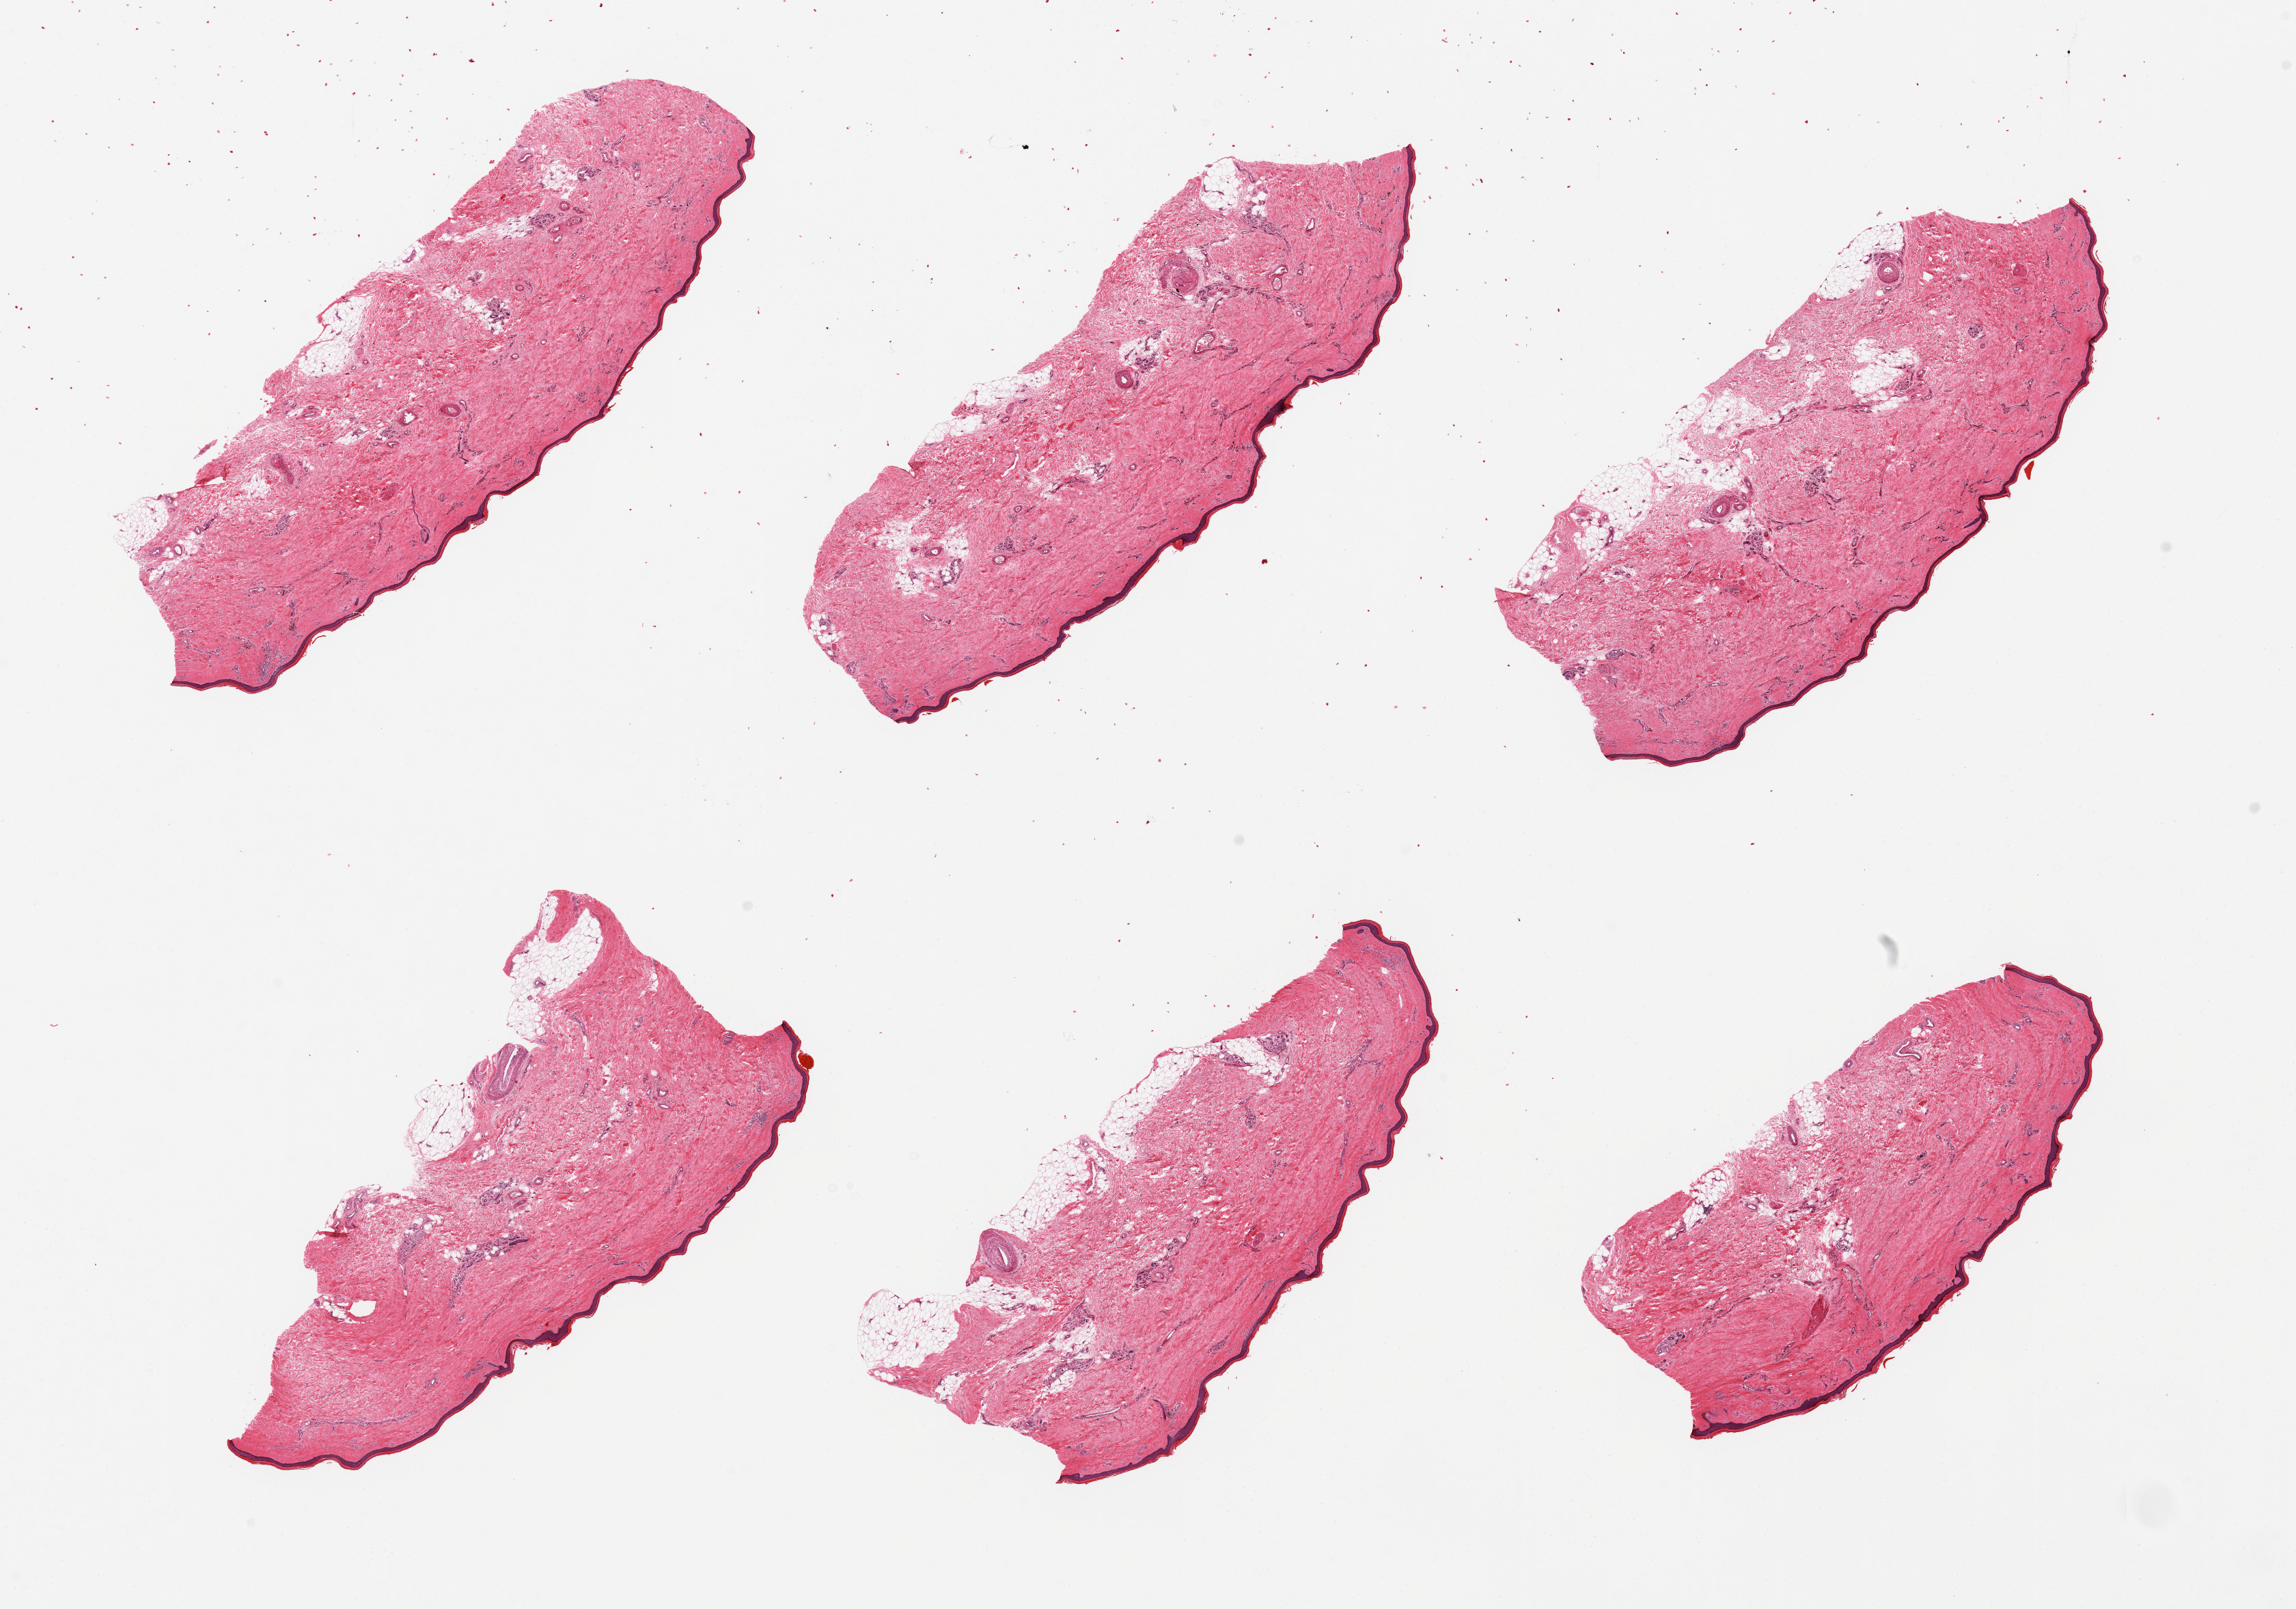
Whole-slide image, haematoxylin and eosin stain, shown as a low-resolution overview of the whole scanned area (about 26.6 x 18.6 mm, acquisition: 20x scan). PAXgene-fixed paraffin-embedded (PFPE) section. Sampled site (target tissue): skin of lower leg. Donor tissue sample. Donor: male.
Pathologist's review note for this sample: 6 pieces, squamous epithelium is ~60 microns thick.